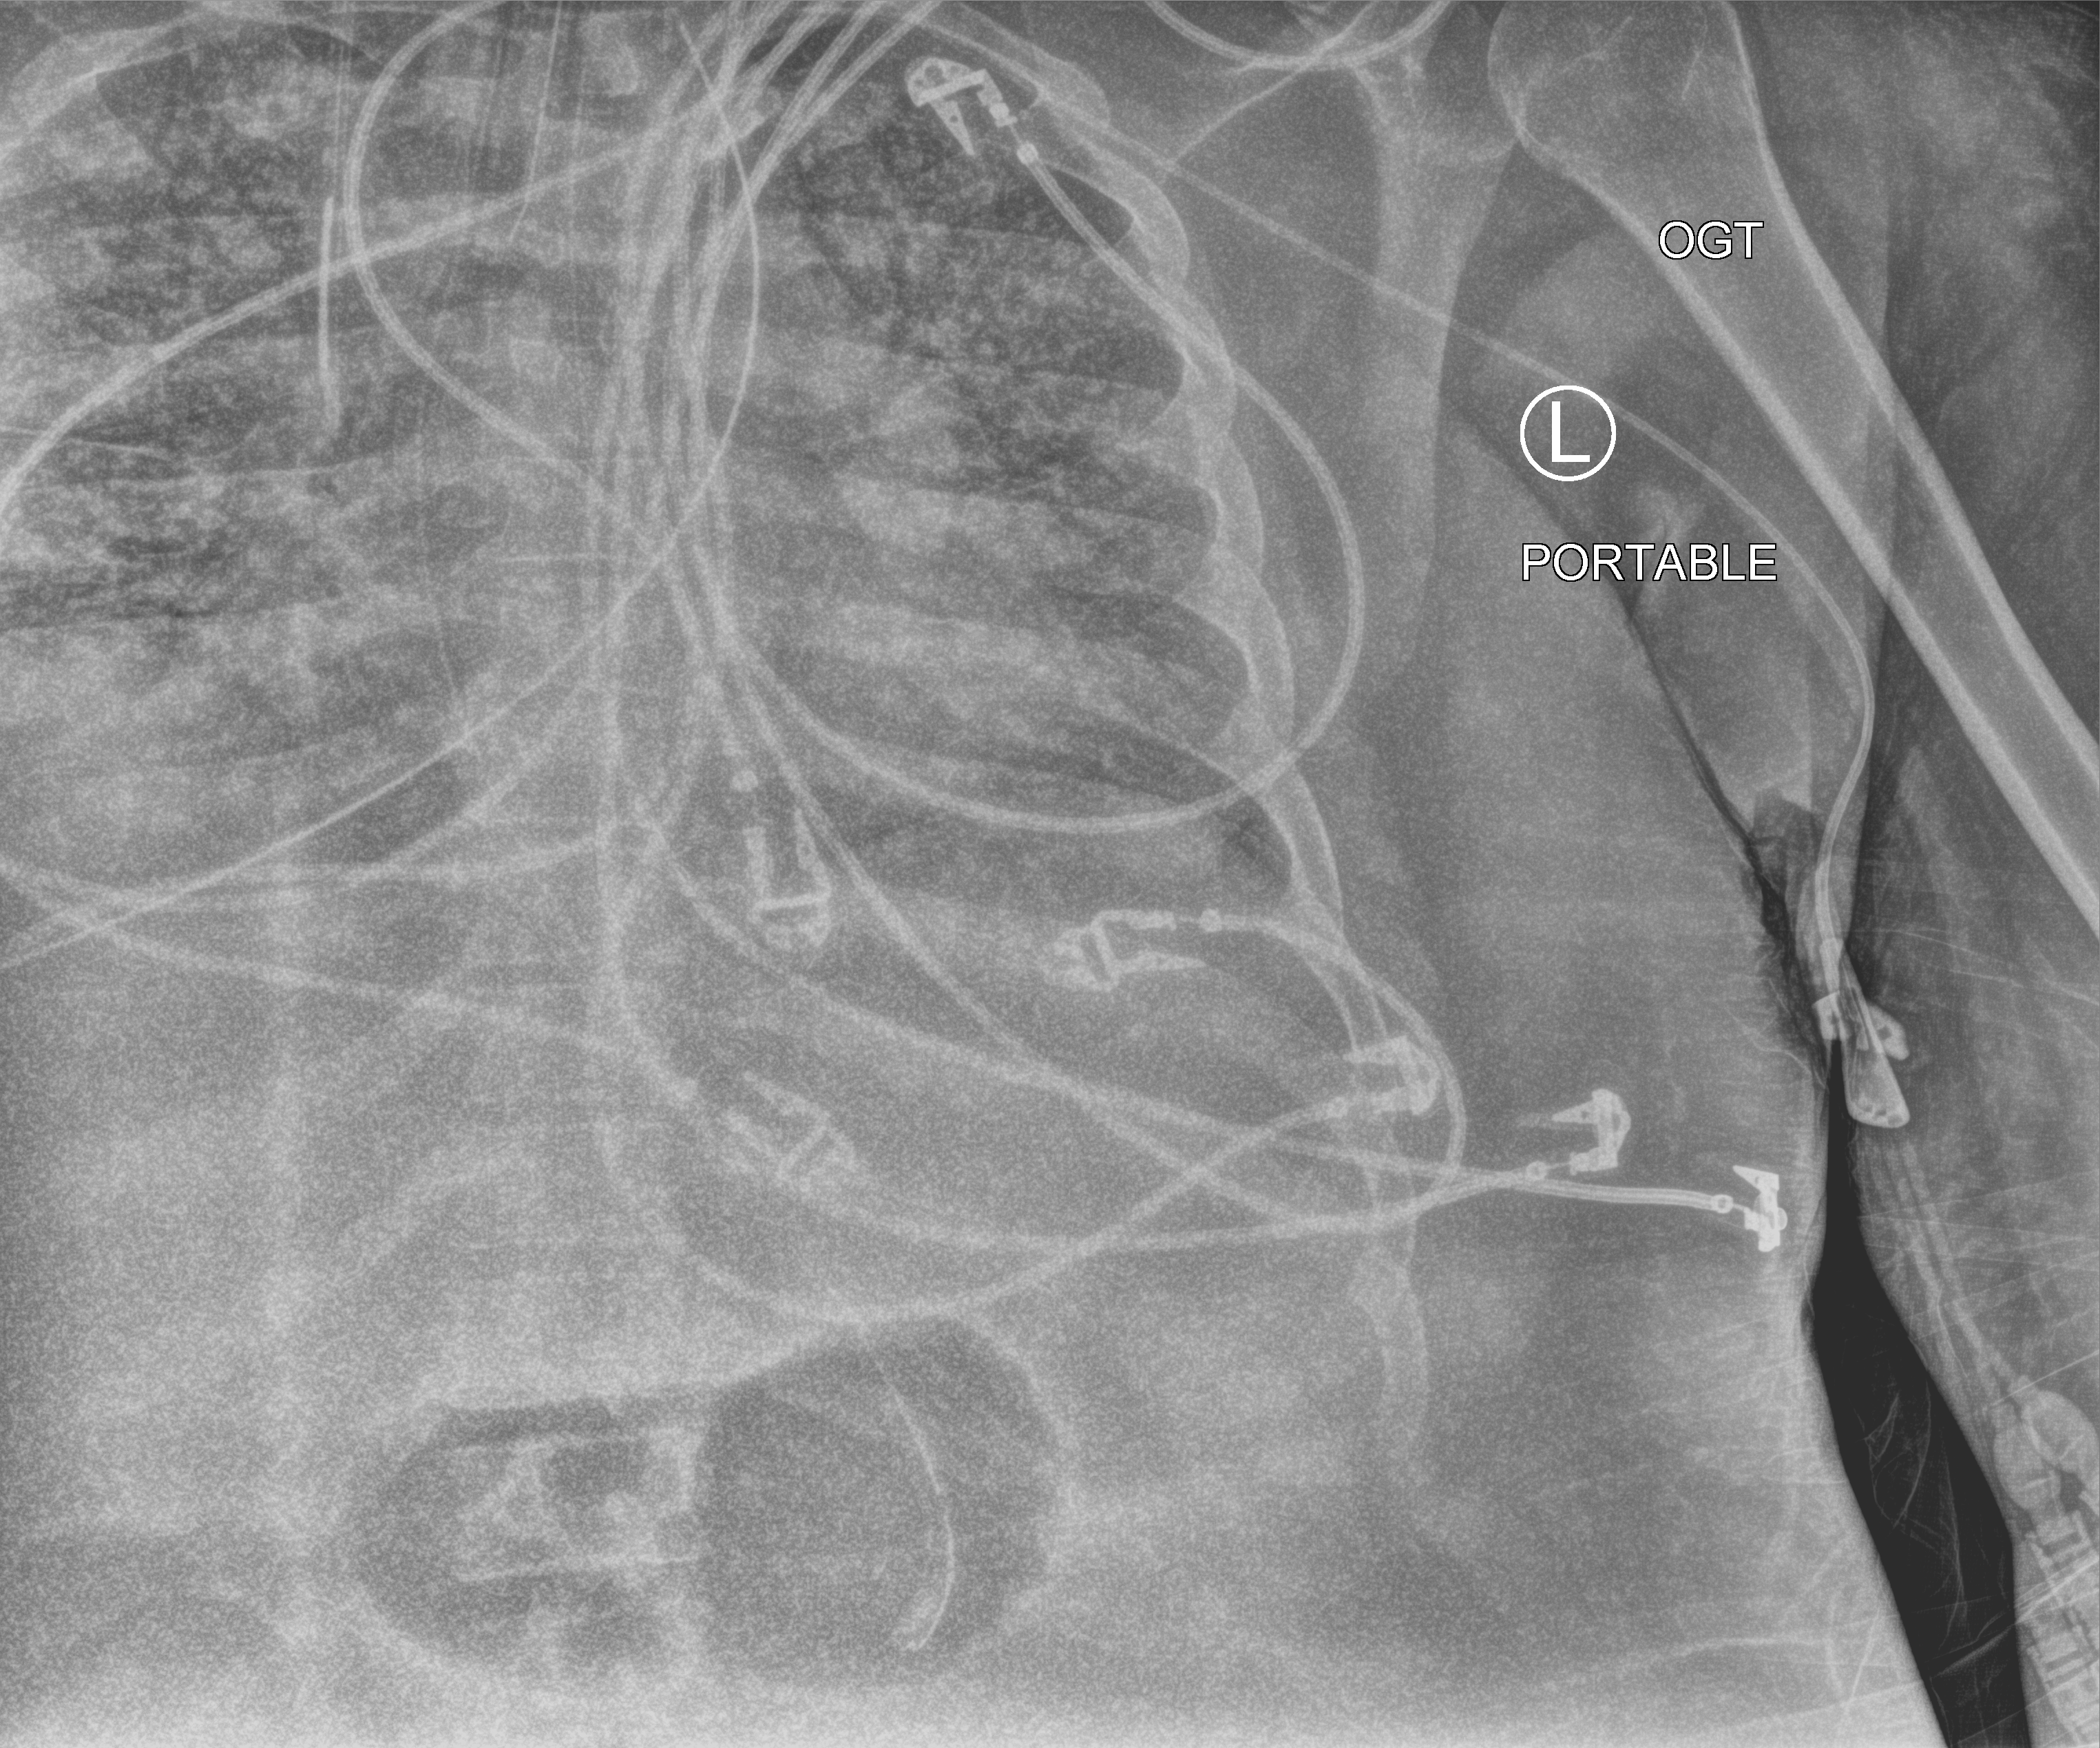
Portable chest radiograph. Patient hospitalised with COVID-19, aged 18–59 years.
Hospital-stay facts (about this admission, not read from this image; timing relative to this image not recorded):
- mechanically ventilated during this hospital stay: yes